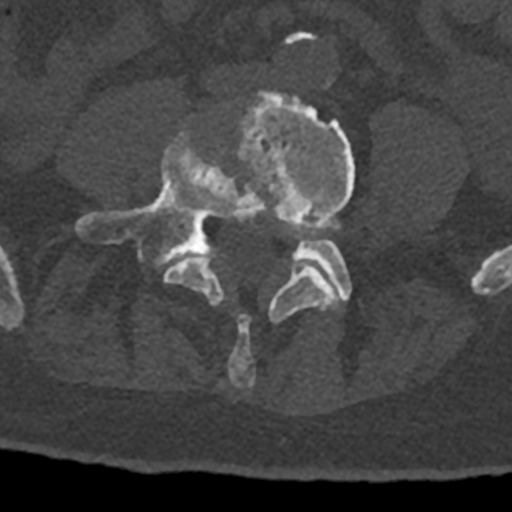
CT including the spine, one axial slice. Position 229 of 797 along the scan axis. 120 kVp. Bone window (W 1800 / L 400 HU). 0.5 mm slice thickness. 512 × 512 image matrix. Patient: male, 74 years. From the clinical record (not read from this slice): primary cancer: renal.
Outlined on this slice (semi-automatic segmentation, software-assisted and operator-edited):
- L4 vertebra: bounding box <163,91,355,387> (left, top, right, bottom; pixels)
- L5 vertebra: <75,133,352,302>